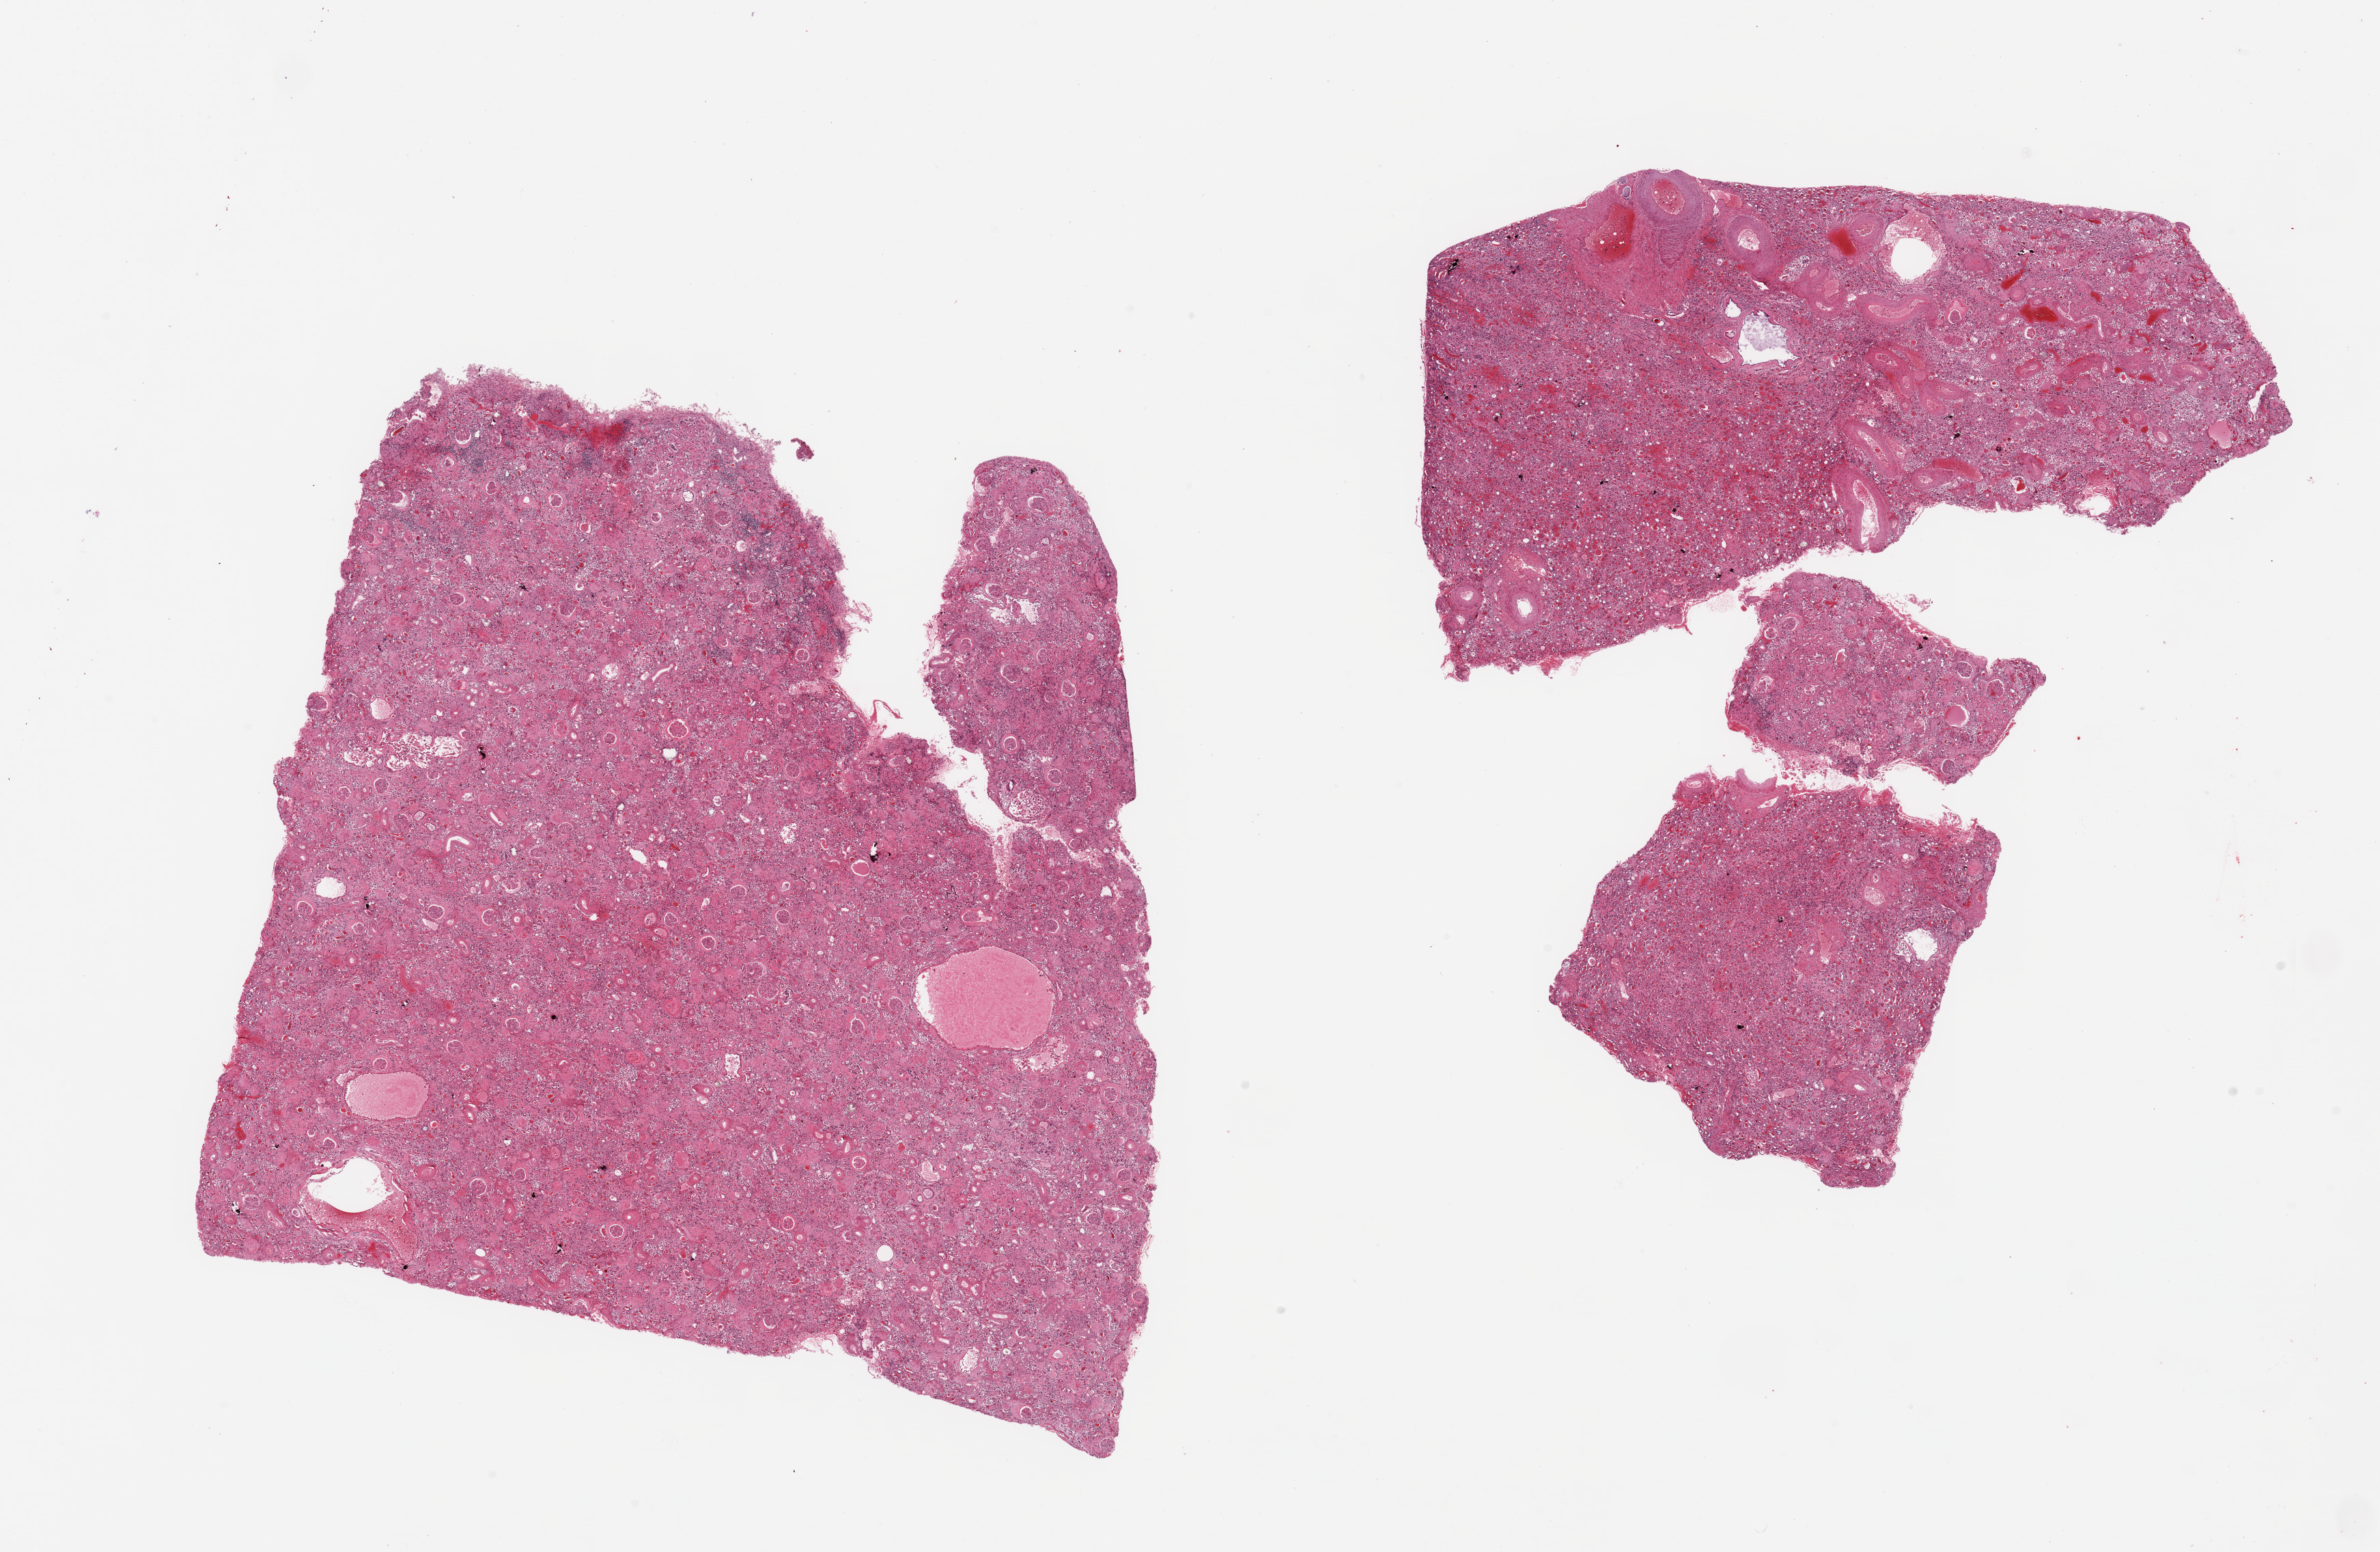
Digitized haematoxylin and eosin-stained section — whole scanned area (about 27.6 x 18.0 mm, from a 20x scan) shown as a low-resolution overview, PAXgene-fixed, paraffin-embedded tissue, section of renal cortex (target tissue), tissue donor sample. Donor: male.
Reviewer comment on this tissue sample: 4 pieces; end stage renal disease.